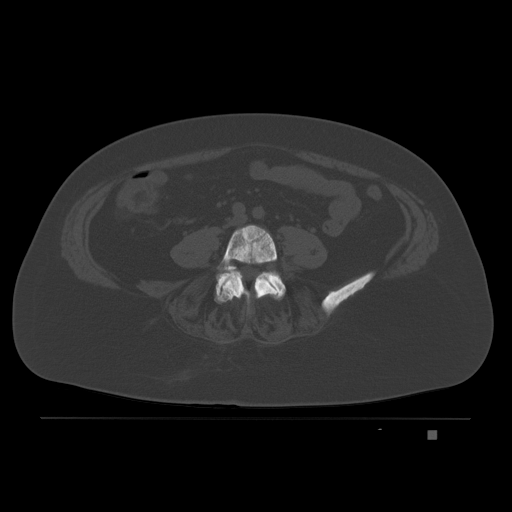
CT including the spine, one axial slice; slice 38 of 221 in the series (ordered by position); bone window (W 1800 / L 400 HU); 3 mm slice thickness; 512 × 512 image matrix, field of view 474 × 474 mm. Patient: female, 63 years. Case-level facts recorded for this patient, not image findings: primary cancer: breast.
Structures marked on this image (semi-automatic segmentation, software-assisted and operator-edited):
- L4 vertebra: bounding box [x1, y1, x2, y2] px = [216, 224, 280, 316]
- L5 vertebra: [215, 271, 286, 302]